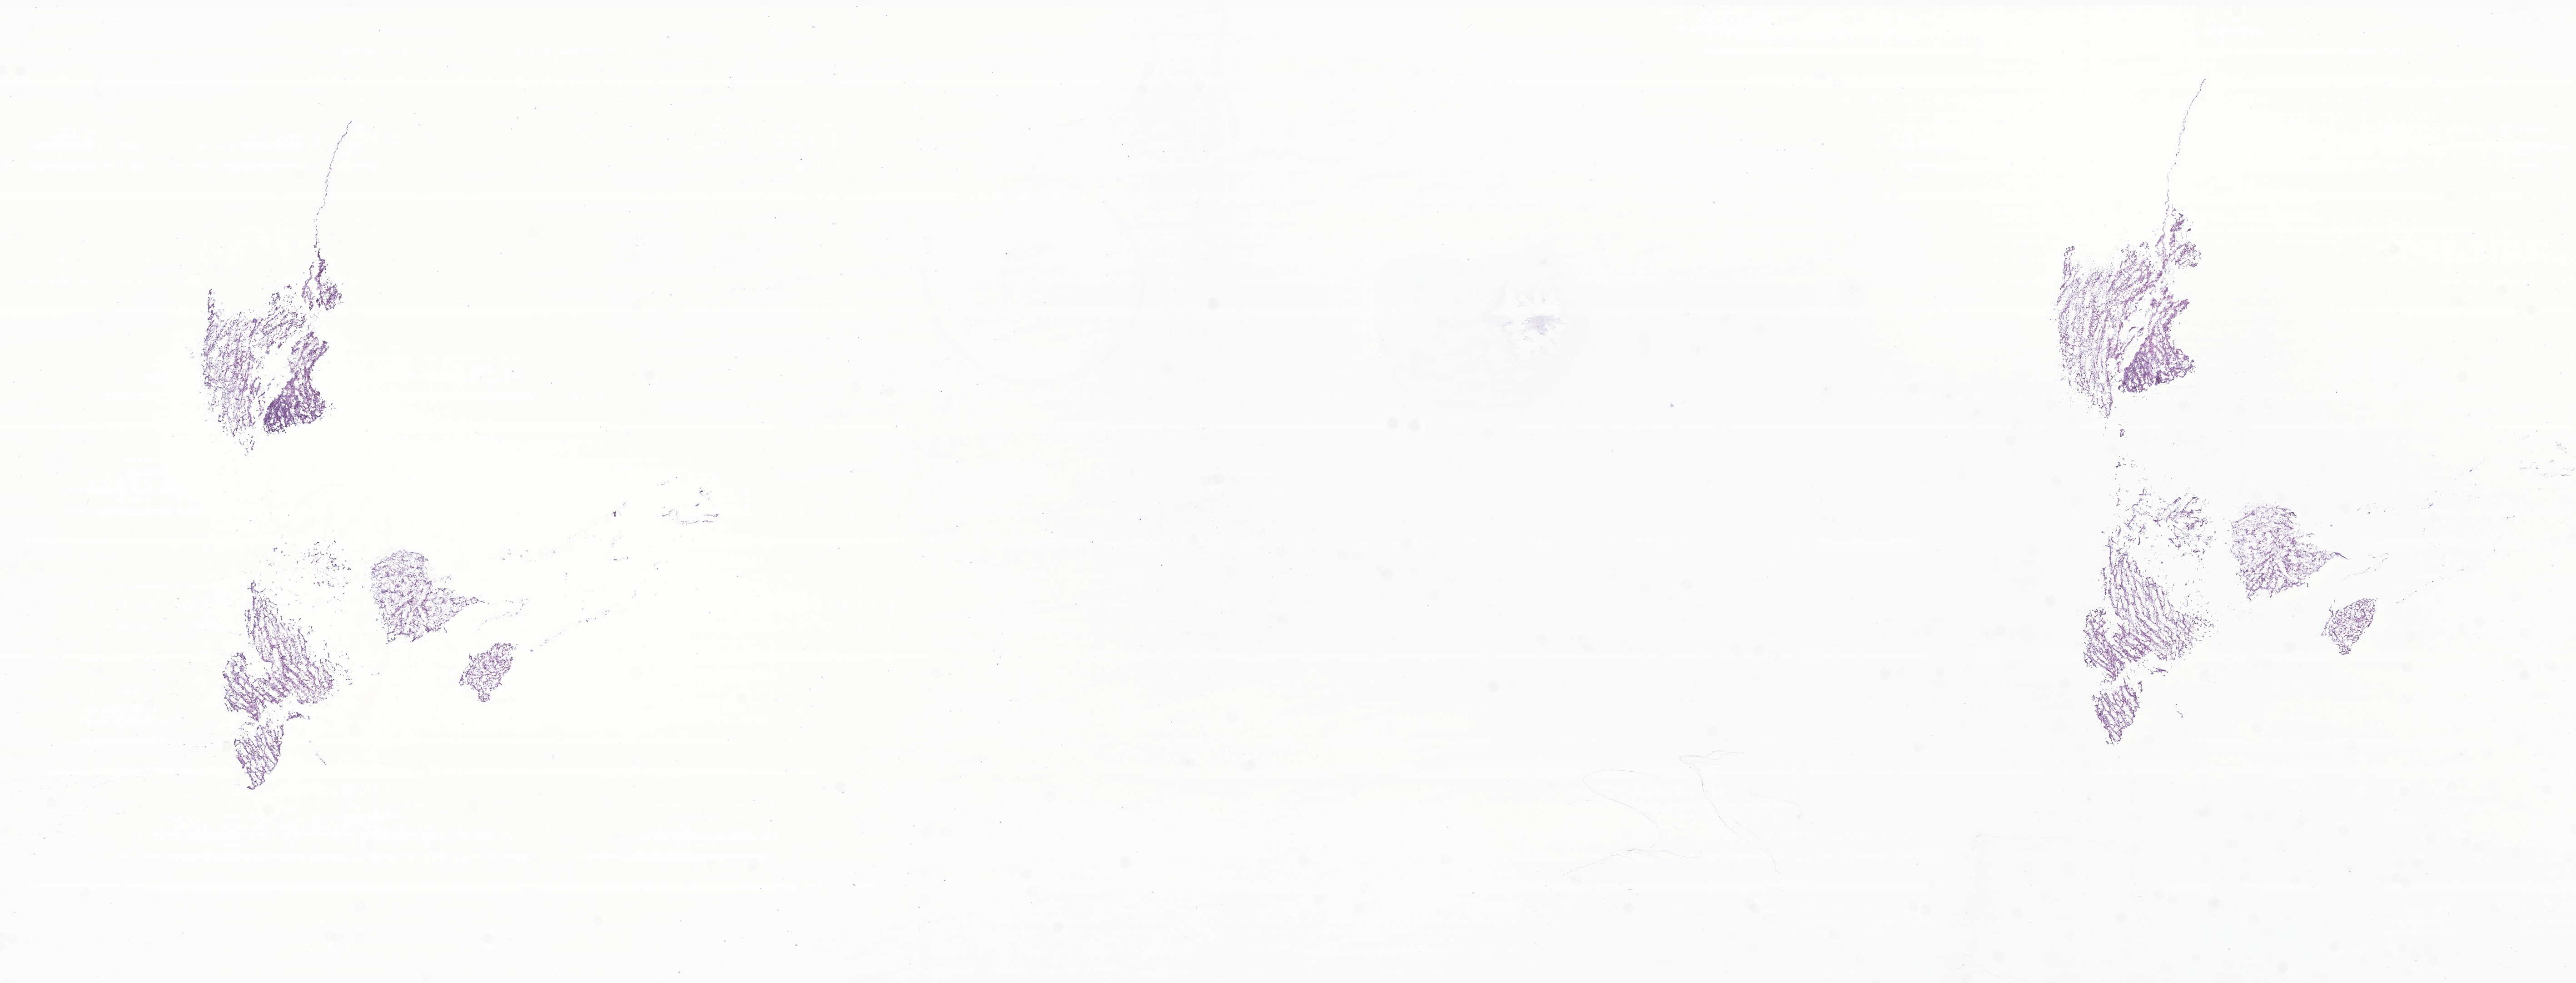
Digitized H&E-stained section of tumor tissue from the orbit, shown as a low-resolution overview of the whole scanned area (about 23.9 x 9.1 mm); frozen section (OCT-embedded). Male patient, age 126 months.
- diagnosis (ICD-O-3 morphology term): Embryonal rhabdomyosarcoma, NOS